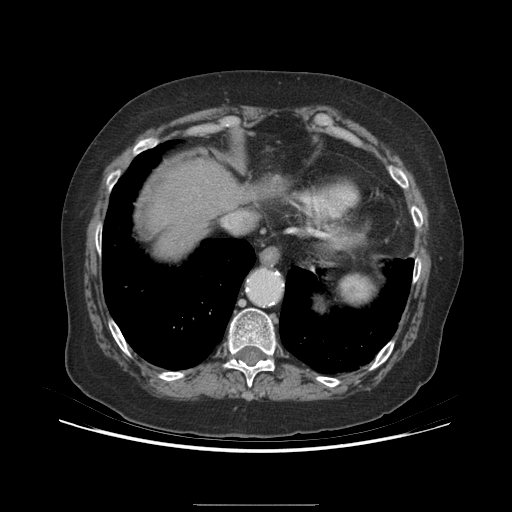
Contrast-enhanced abdominal CT (liver protocol), one axial slice; soft-tissue window (W 400 / L 40 HU); 2.5 mm slice thickness; 512 × 512 image matrix, field of view 400 × 400 mm. Case-level facts recorded for this patient, not image findings: diagnosis: hepatocellular carcinoma (patient treated with transarterial chemoembolisation; whether this scan precedes or follows treatment is not stated here); TNM stage (as recorded): Stage-I; Child-Pugh class: A; tumour differentiation: moderately differentiated; tumour nodularity: uninodular.
Structures marked on this image (semi-automatically segmented with operator editing):
- abdominal aorta: box from (x=250, y=270) to (x=280, y=304) px
- liver parenchyma outside the tumour (the mass and vessels are separate outlines, so this box may not span the whole liver): (x=146, y=158)–(x=254, y=254)